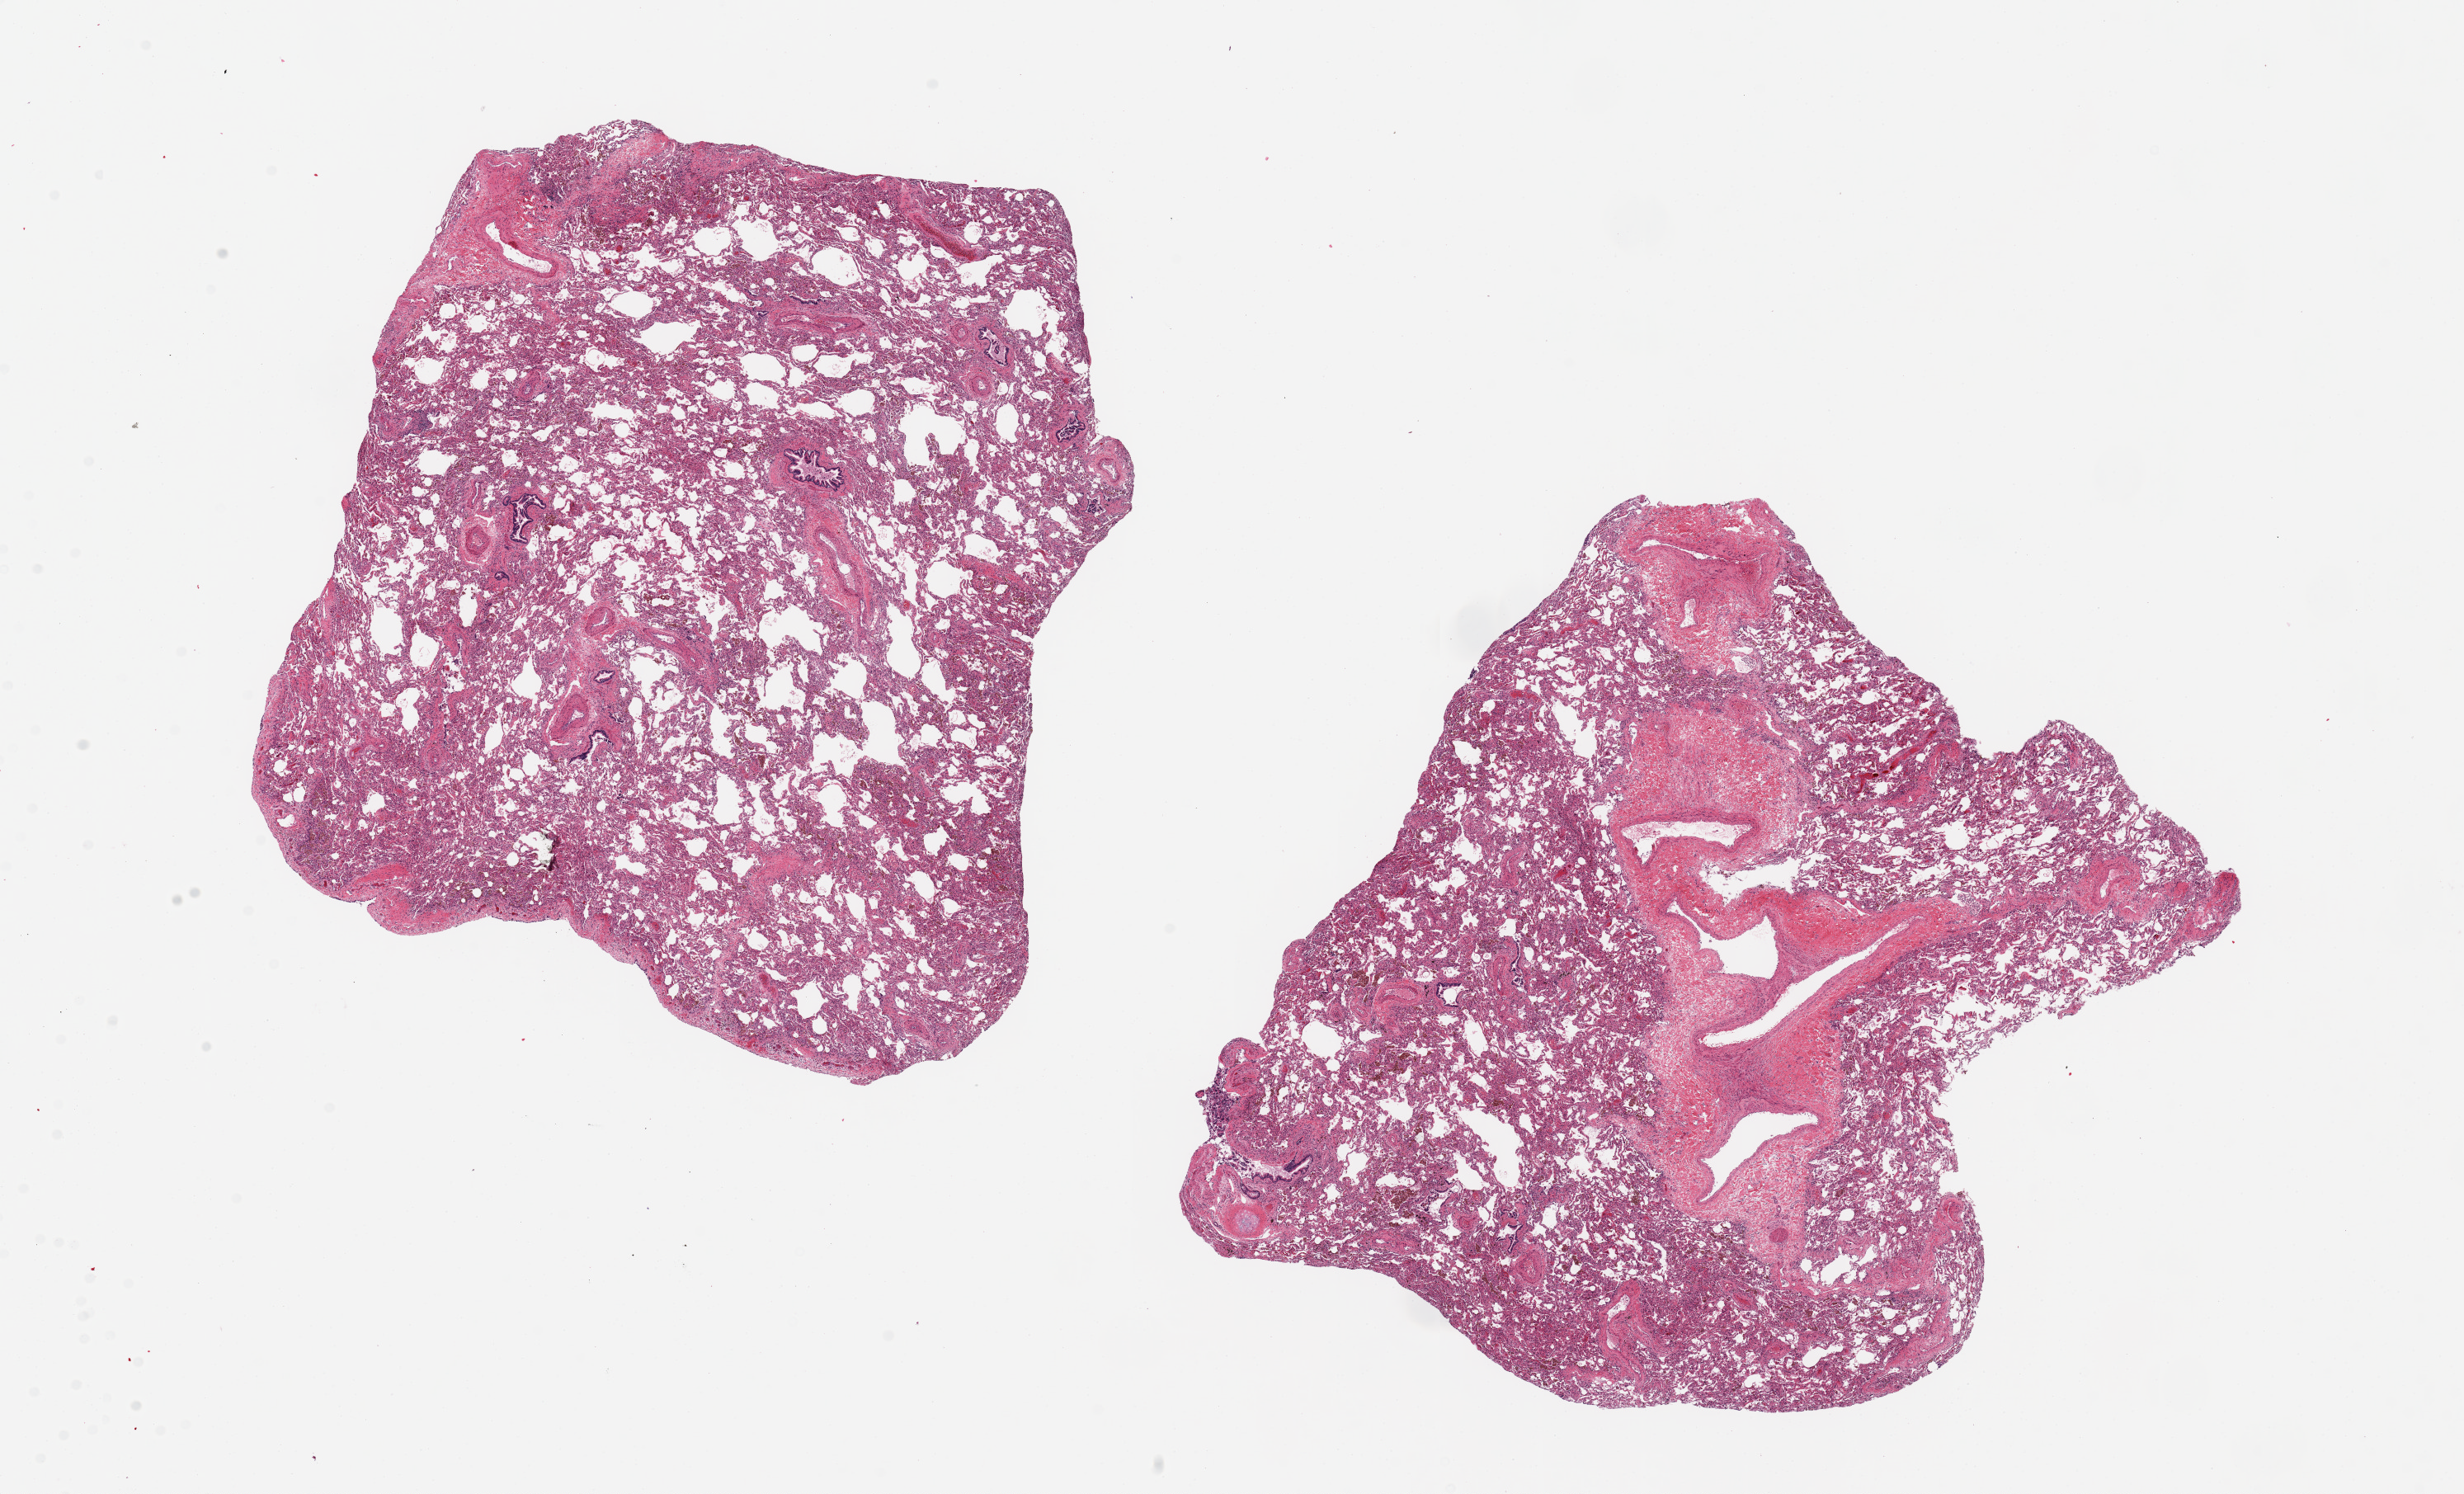
Haematoxylin and eosin whole-slide image — whole scanned area (about 23.6 x 14.3 mm, slide scanned at 20x) shown as a low-resolution overview. PAXgene-fixed paraffin-embedded (PFPE) section. Sampled site (target tissue): lung. Donor tissue sample. Donor: female.
Reviewer comment on this tissue sample: 2 pieces, 8x8 & 9x9mm.